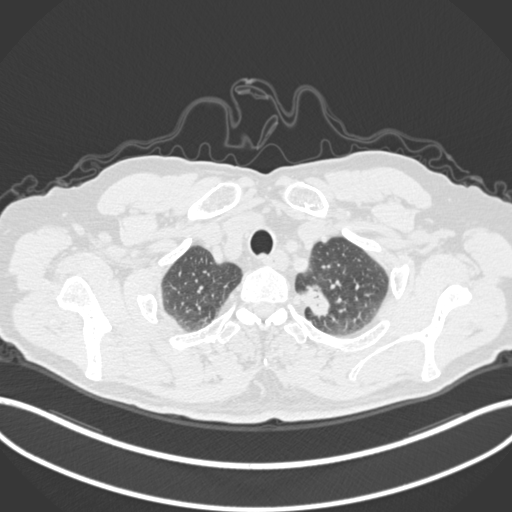
Chest CT, one axial slice; position 284 of 306 along the scan axis; reconstruction kernel B30f; lung window (W 1500 / L -600 HU); 512 × 512 image matrix. Male patient, age 64 years. From the clinical record (not read from this slice): clinical TNM (as recorded): T1c N0 M0.
Outlined on this slice (bounding box drawn by a radiologist):
- lung tumour (recorded histology: adenocarcinoma): bounding box <298,282,333,321> (left, top, right, bottom; pixels)